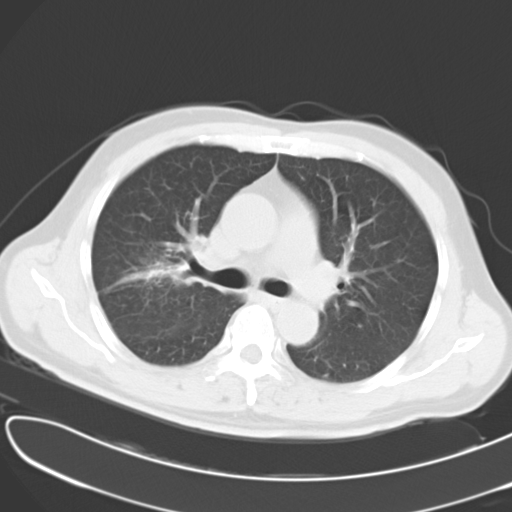
Chest CT, one axial slice; position 23 of 37 along the scan axis; 120 kVp; lung window (W 1500 / L -600 HU); 8 mm slice thickness; 512 × 512 image matrix, field of view 353 × 353 mm. Male patient, age 53 years. Case-level facts recorded for this patient, not image findings: clinical TNM (as recorded): T2 N1 M0.
Outlined on this slice (rectangle marked by the reading radiologist):
- lung tumour (recorded histology: adenocarcinoma): bounding box (x1, y1, x2, y2) in pixels: (103, 256, 197, 293)